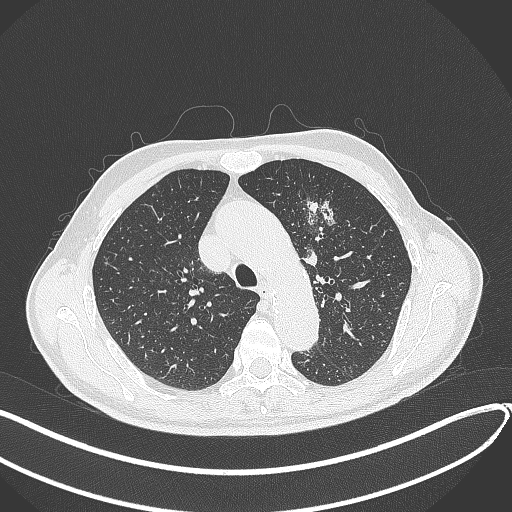
Chest CT, one axial slice. Slice 301 of 459 in the series (ordered by position). 120 kVp. Lung window (W 1500 / L -600 HU). 512 × 512 image matrix, field of view 400 × 400 mm. Male patient, age 74 years. Case-level facts recorded for this patient, not image findings: clinical TNM (as recorded): T2b N0 M1c.
Annotated regions visible in this slice (bounding box drawn by a radiologist):
- lung tumour (recorded histology: adenocarcinoma): box from (x=306, y=200) to (x=337, y=244) px